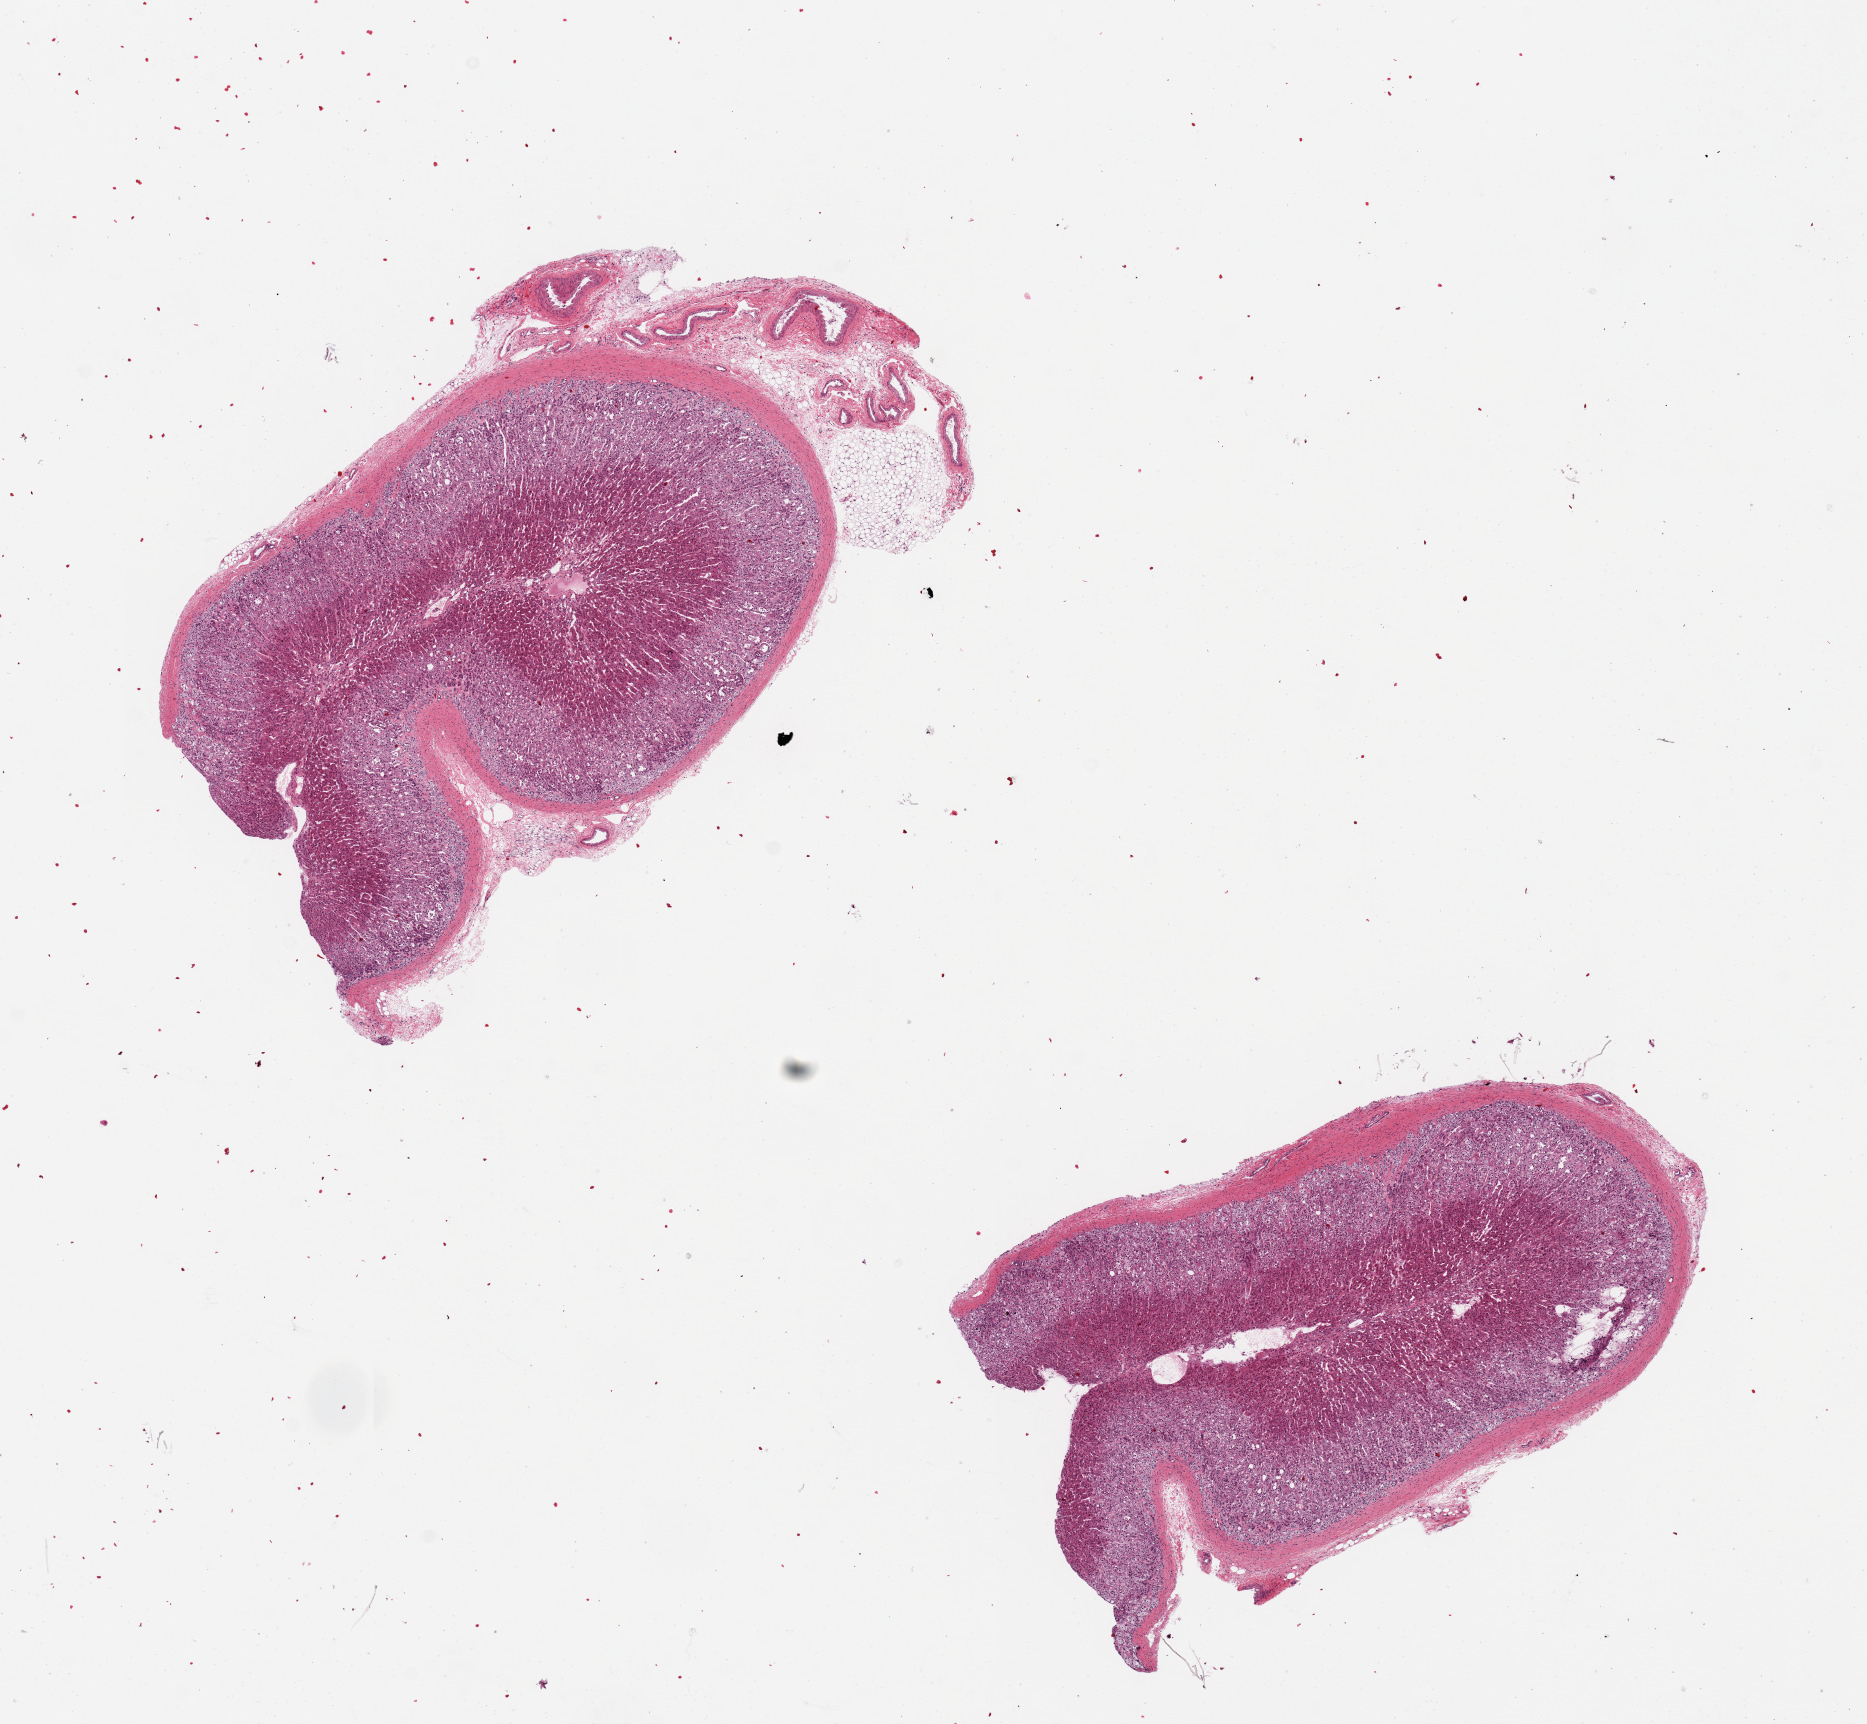
H&E whole-slide image, brightfield — a low-resolution overview of the entire scanned area, about 14.8 x 13.6 mm; PAXgene-fixed paraffin-embedded (PFPE) section; sampled site (target tissue): adrenal gland; tissue donor sample. Donor: female.
Reviewer comment on this tissue sample: 2 pieces, 3.6 x 1.2mm attachment of fat and vessels on one piece.